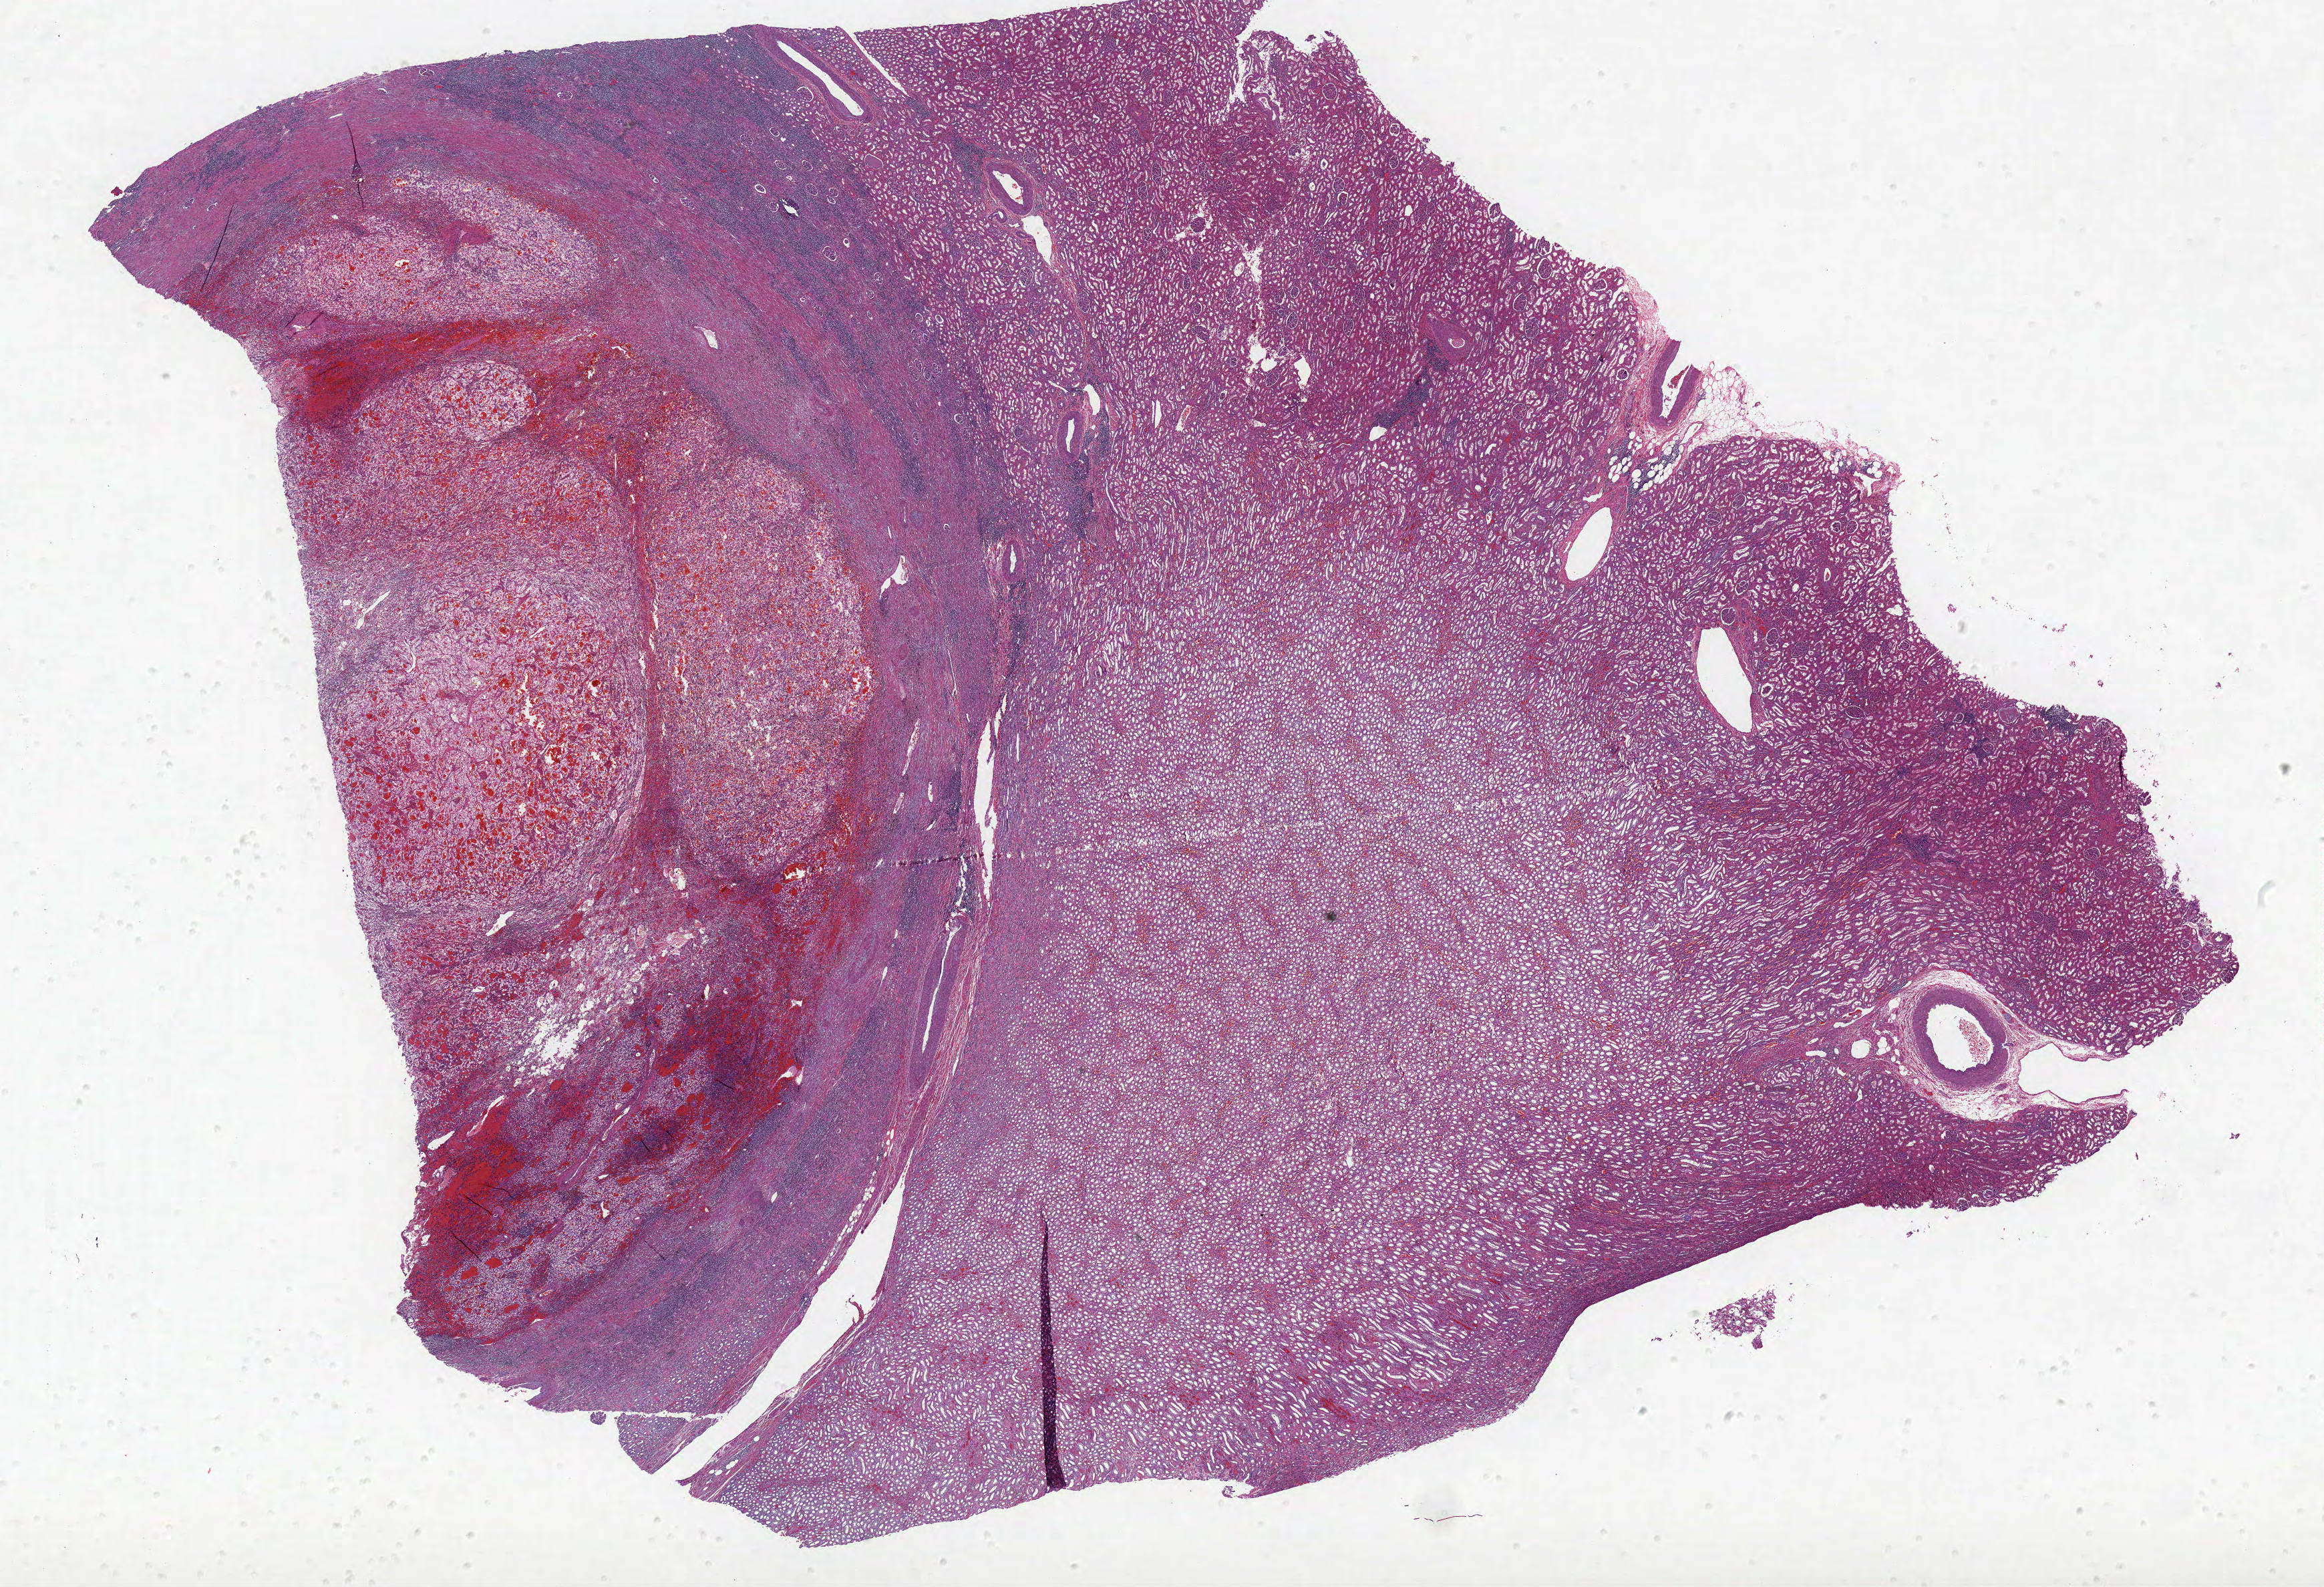
Whole-slide histology image, H&E, low-resolution overview of the scanned area, about 27.8 x 19.0 mm (from a 40x scan); FFPE section; kidney, primary tumour sample. Patient: male, age at initial diagnosis 72 years. Histologic grade: G2 (moderately differentiated).
* AJCC pathologic stage: I
* lymph nodes positive (case pathology): 0 of 1 examined
* histologic diagnosis: Clear cell adenocarcinoma, NOS